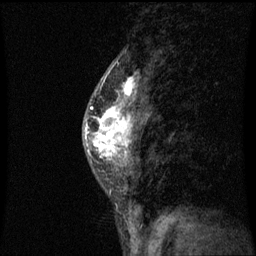
Breast MRI (dynamic contrast-enhanced), one sagittal slice. Slice 28 of 60 in the series (ordered by position). Dynamic contrast-enhanced series, image 2 of 3 at this slice position (ordered by acquisition). 1.5 T. TE 4.2 ms, TR 8.9 ms. 256 × 256 image matrix, field of view 200 × 200 mm. Patient: female, 50 years. From the clinical record (not read from this slice): setting: breast cancer imaged before/during neoadjuvant chemotherapy; receptor status: triple-negative.
Structures marked on this image (semi-automatically segmented with operator editing):
- analysis volume of interest (the breast-tissue region the enhancement analysis was run in; not a lesion): bounding box <84,80,147,171> (left, top, right, bottom; pixels)
- tumour enhancement mask (voxels above the 70 % enhancement threshold inside the analysis volume of interest): <86,80,137,163>